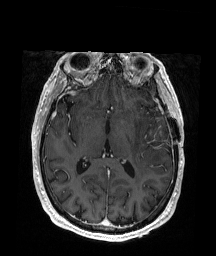
Brain MRI from a brain-tumour surgery series, one axial slice. Position 96 of 176 along the scan axis. T1-weighted post-contrast. 1 mm slice thickness. 216 × 256 image matrix, field of view 219 × 260 mm. Case-level facts recorded for this patient, not image findings: histopathology: Glioblastoma; WHO grade: 4; IDH mutation: no; tumour location: Left Frontal.
Annotated regions visible in this slice (manually delineated by an expert):
- tumour: bounding box <151,129,163,136> (left, top, right, bottom; pixels)